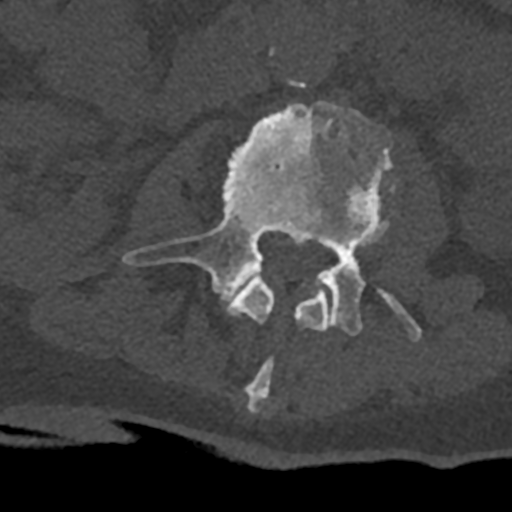
CT including the spine, one axial slice. Slice 339 of 797 in the series (ordered by position). 120 kVp. Bone window (W 1800 / L 400 HU). 0.5 mm slice thickness. 512 × 512 image matrix. Patient: male, 74 years. From the clinical record (not read from this slice): primary cancer: renal.
Outlined on this slice (semi-automatically segmented with operator editing):
- L2 vertebra: bounding box <228,272,330,413> (left, top, right, bottom; pixels)
- L3 vertebra: <122,101,421,341>